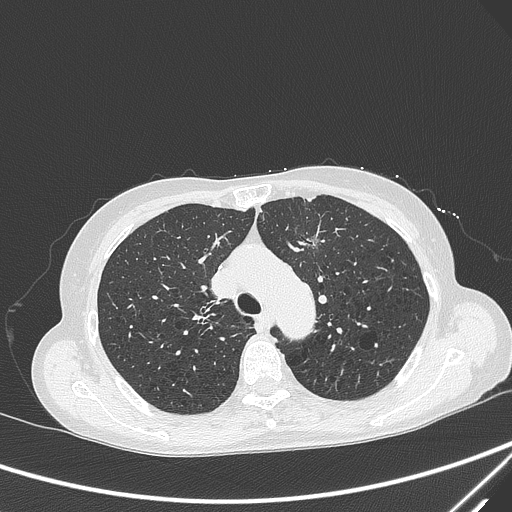
Chest CT, one axial slice. Position 217 of 299 along the scan axis. Lung window (W 1500 / L -600 HU). 1 mm slice thickness. 512 × 512 image matrix, field of view 350 × 350 mm. Female patient, age 71 years. From the clinical record (not read from this slice): clinical TNM (as recorded): T1c N0 M0; histopathological grade: G2-3.
Structures marked on this image (bounding box drawn by a radiologist):
- lung tumour (recorded histology: adenocarcinoma): bounding box <304,227,321,259> (left, top, right, bottom; pixels)